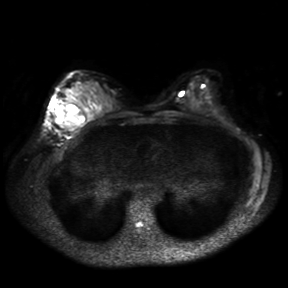
Breast MRI, one axial slice. Position 17 of 30 along the scan axis. Diffusion-weighted series; image 2 of 4 stored at this slice position (different b-values; order by instance number). 3 T. 4 mm slice thickness. 288 × 288 image matrix. Female patient.
Annotated regions visible in this slice (outlined manually by an expert reader):
- tumour on diffusion-weighted imaging: bounding box <51,99,75,131> (left, top, right, bottom; pixels)